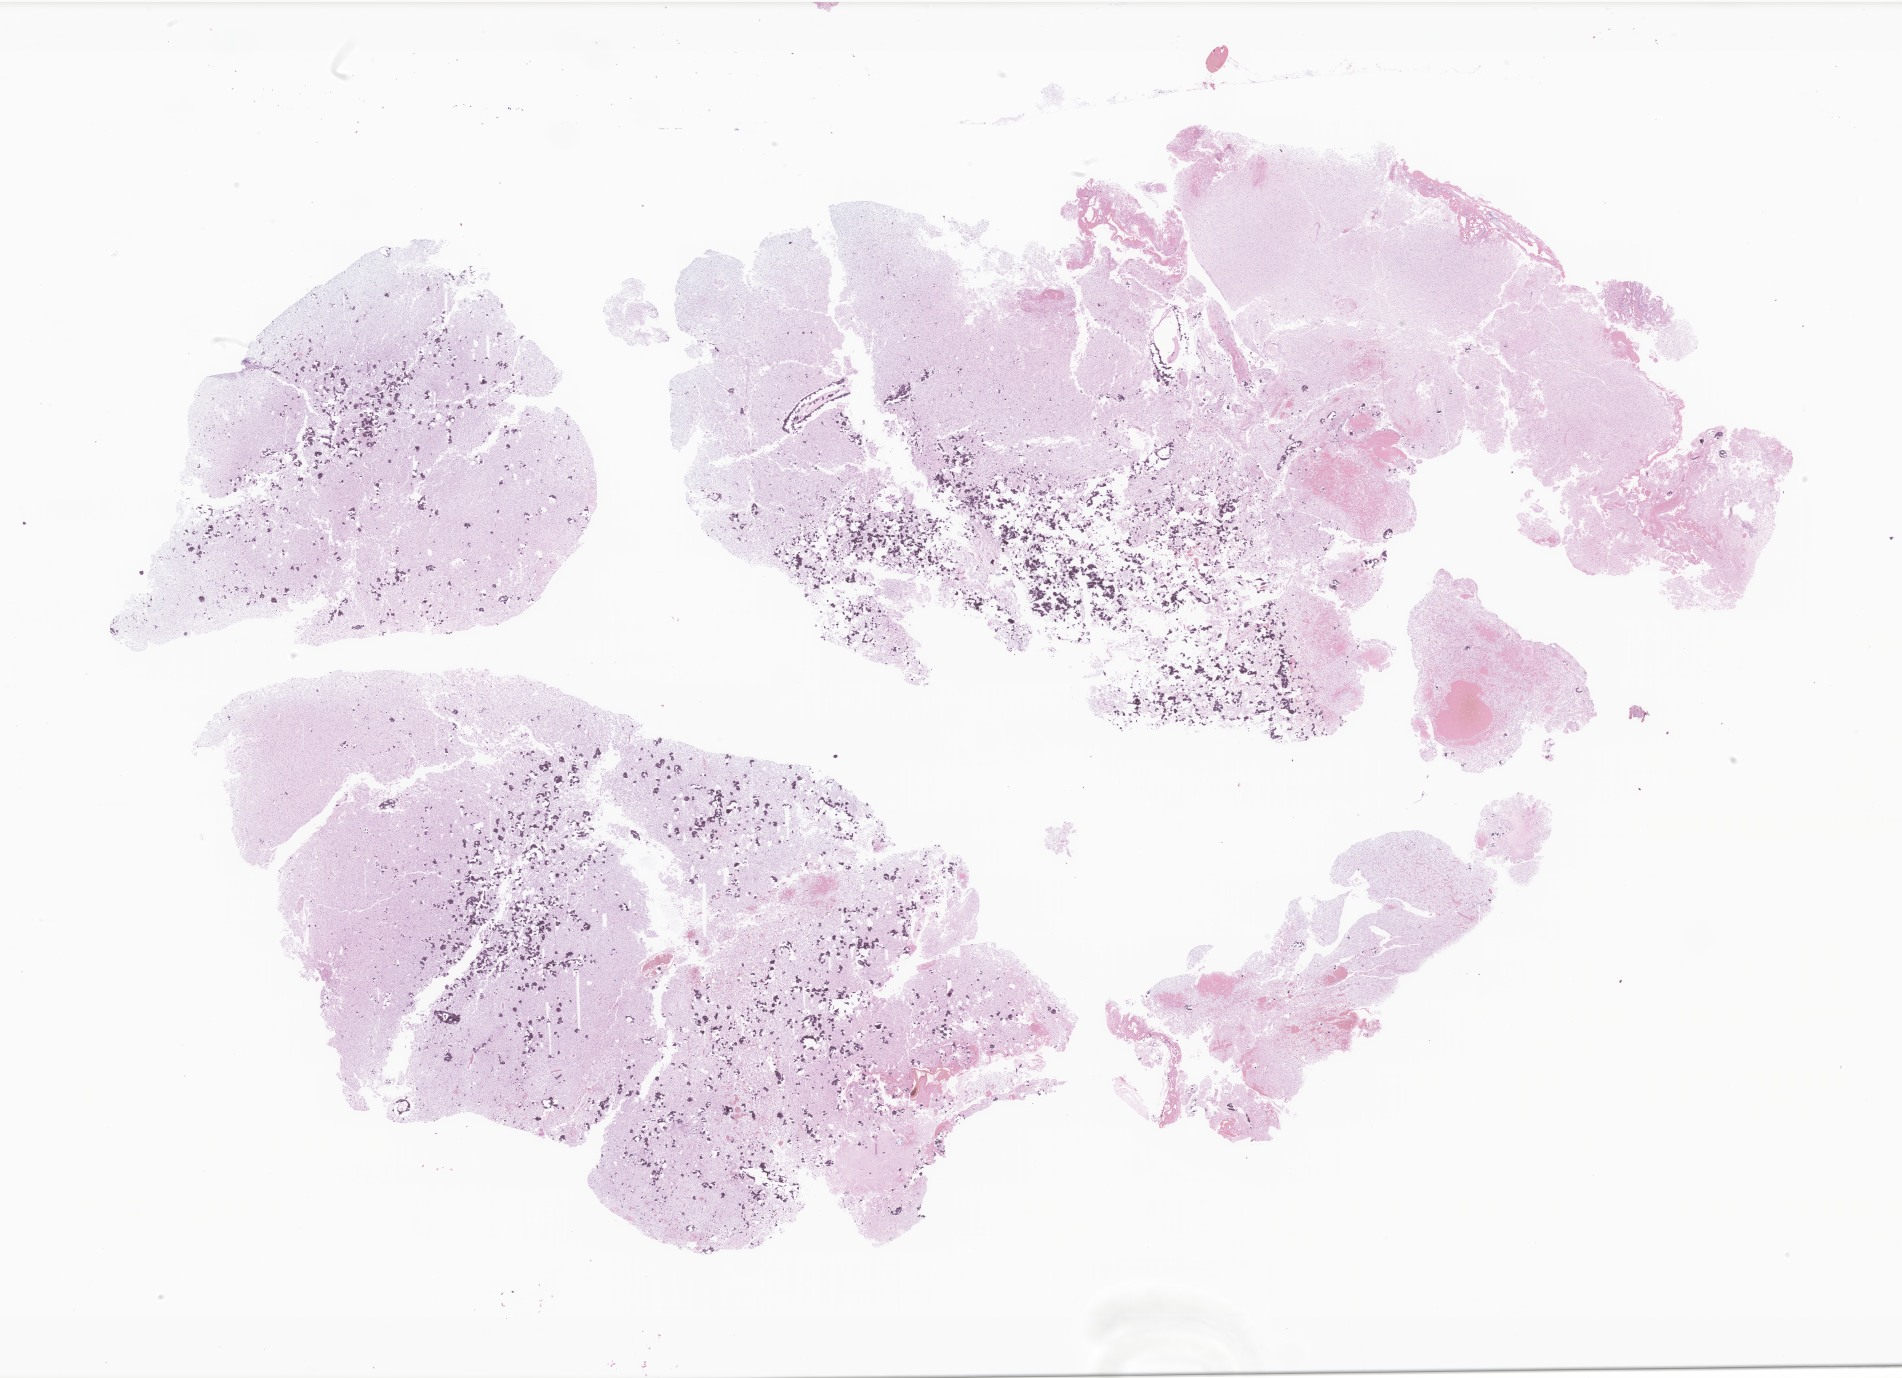
Whole-slide image, H&E stain of tumor tissue from the temporal lobe, a low-resolution overview of the entire scanned area, about 32.1 x 23.2 mm. FFPE section. Patient female; age 59 months (4 years 11 months).
Recorded diagnosis: Dysembryoplastic neuroepithelial tumor.